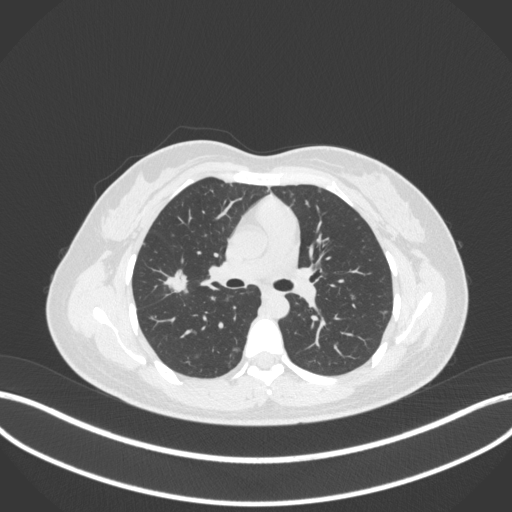
Chest CT, one axial slice. Position 200 of 214 along the scan axis. Reconstruction kernel B31f. Lung window (W 1500 / L -600 HU). 512 × 512 image matrix, field of view 400 × 400 mm. Female patient, age 33 years. Case-level facts recorded for this patient, not image findings: clinical TNM (as recorded): T1c N0 M0; histopathological grade: G2-G3.
Structures marked on this image (rectangle marked by the reading radiologist):
- lung tumour (recorded histology: adenocarcinoma): box from (x=163, y=268) to (x=192, y=298) px